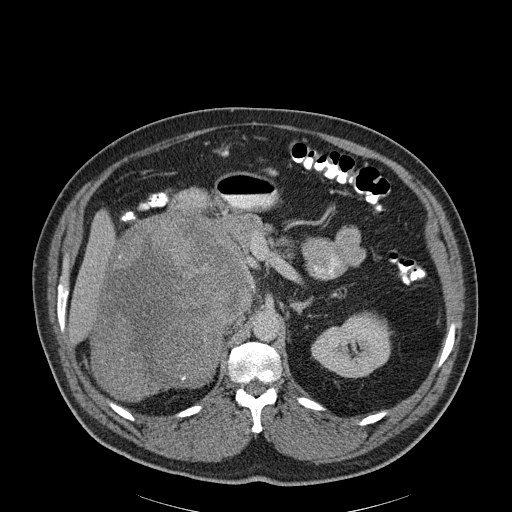
Contrast-enhanced abdominal CT, one axial slice; position 128 of 186 along the scan axis; reconstruction kernel B30f; 120 kVp; soft-tissue window (W 400 / L 40 HU); 512 × 512 image matrix. Patient: male, 56 years. From the clinical record (not read from this slice): diagnosis: adrenocortical carcinoma; tumour side: right adrenal; tumour size at pathology: 18 cm; Ki-67 index: 2 %.
Outlined on this slice (semi-automatic segmentation, software-assisted and operator-edited):
- mass: bounding box [x1, y1, x2, y2] px = [92, 214, 247, 398]